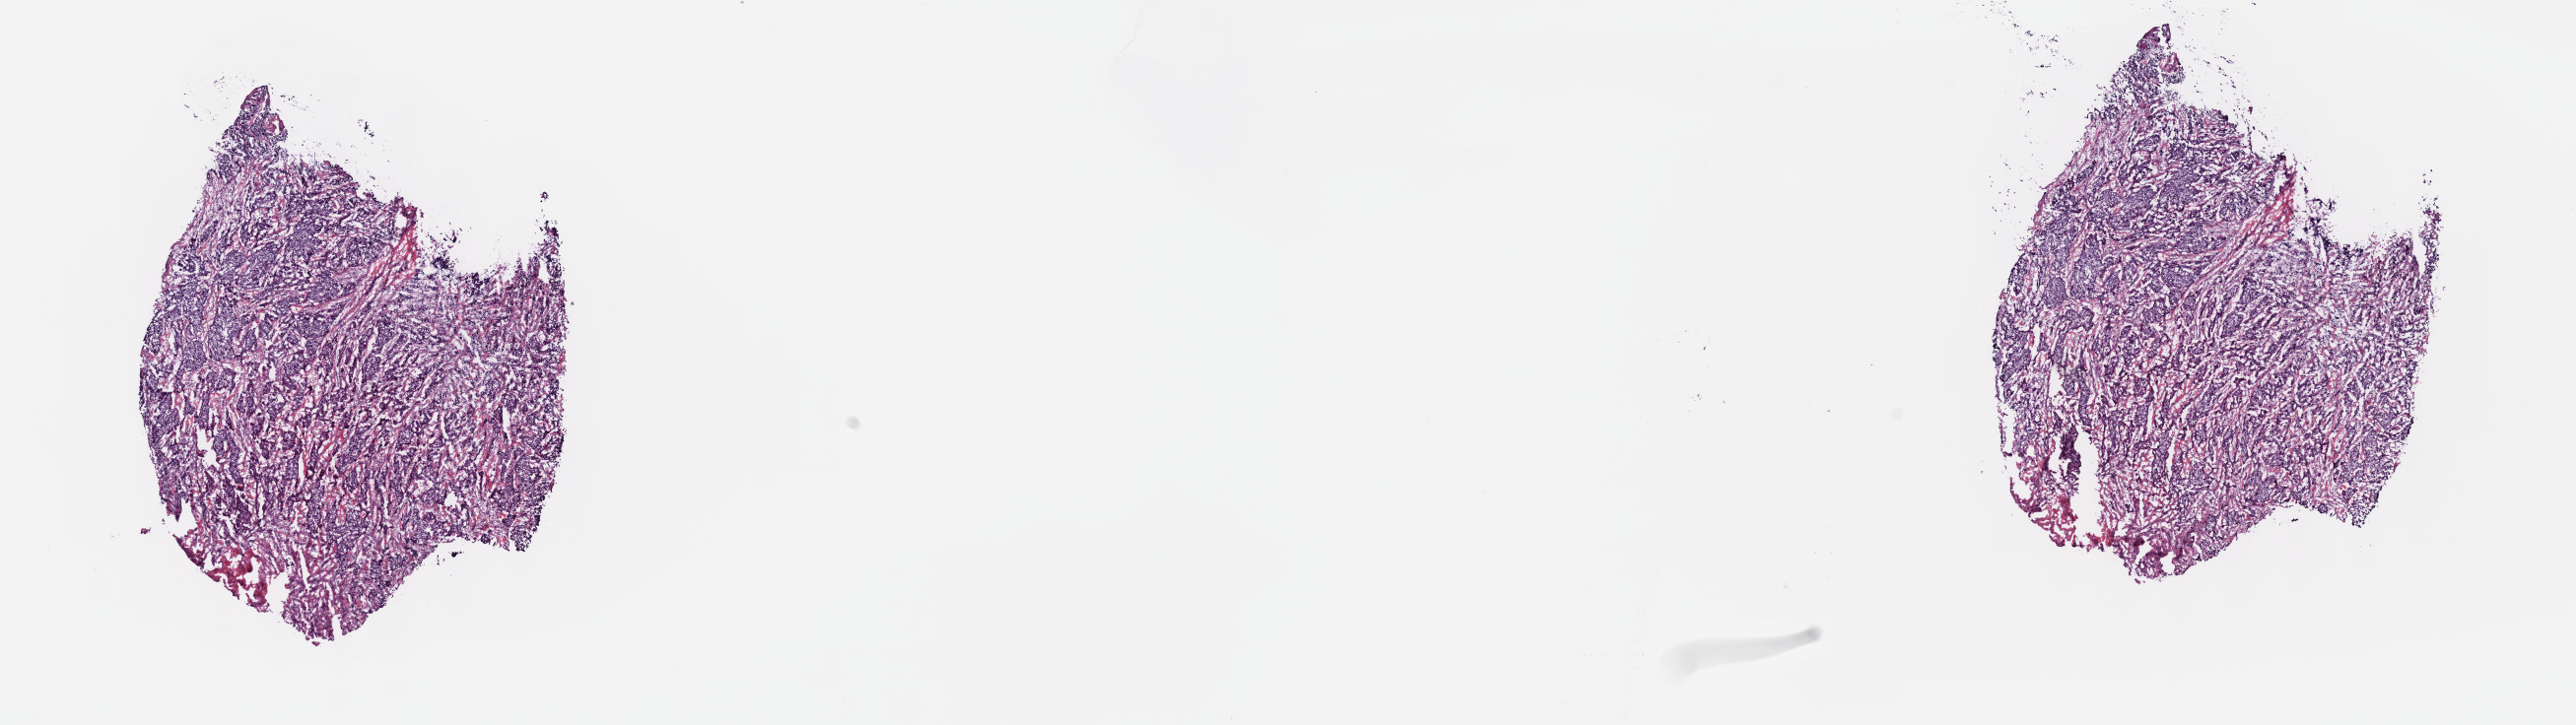
Hematoxylin and eosin (H&E) stained whole-slide image, shown as a low-resolution overview of the whole scanned area (about 21.1 x 6.0 mm), frozen section from the top of the tissue portion, sample: primary tumour, cervix. Patient: female, age at initial diagnosis 57 years. Histologic grade: G3 (poorly differentiated). Composition of this section per pathologist review: tumour cells 80%, tumour nuclei 80%, normal cells 0%, stromal cells 20%, necrosis 0%. Infiltration values recorded for this section: lymphocyte infiltration 5%, monocyte infiltration 5%, neutrophil infiltration 0%.
Histologic diagnosis: Squamous cell carcinoma, NOS (cervix uteri). Lymph nodes positive (case pathology): 4 of 28 examined.